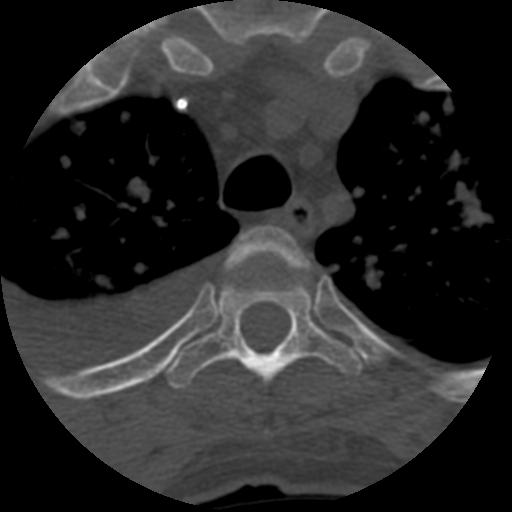
CT including the spine, one axial slice. Slice 476 of 708 in the series (ordered by position). 120 kVp. One of 3 acquisitions stored at this slice position. Bone window (W 1800 / L 400 HU). 512 × 512 image matrix, field of view 160 × 160 mm. Patient age 55 years. From the clinical record (not read from this slice): primary cancer: colon.
Outlined on this slice (semi-automatically segmented with operator editing):
- T3 vertebra: box from (x=228, y=226) to (x=308, y=271) px
- T4 vertebra: (x=165, y=260)–(x=363, y=388)